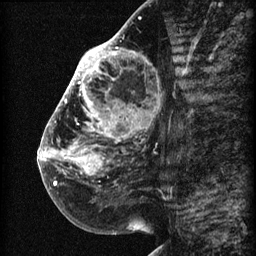
Breast MRI (dynamic contrast-enhanced), one sagittal slice; position 30 of 60 along the scan axis; 3 images stored at this slice position (order not interpretable as contrast timing); 1.5 T; TE 4.2 ms, TR 22.7 ms; 256 × 256 image matrix, field of view 180 × 180 mm. Patient: female, 48 years. From the clinical record (not read from this slice): setting: breast cancer imaged before/during neoadjuvant chemotherapy; receptor status: triple-negative.
Annotated regions visible in this slice (semi-automatic segmentation, software-assisted and operator-edited):
- analysis volume of interest (the breast-tissue region the enhancement analysis was run in; not a lesion): bounding box <44,30,173,207> (left, top, right, bottom; pixels)
- tumour enhancement mask (voxels above the 90 % enhancement threshold inside the analysis volume of interest): <44,30,147,186>